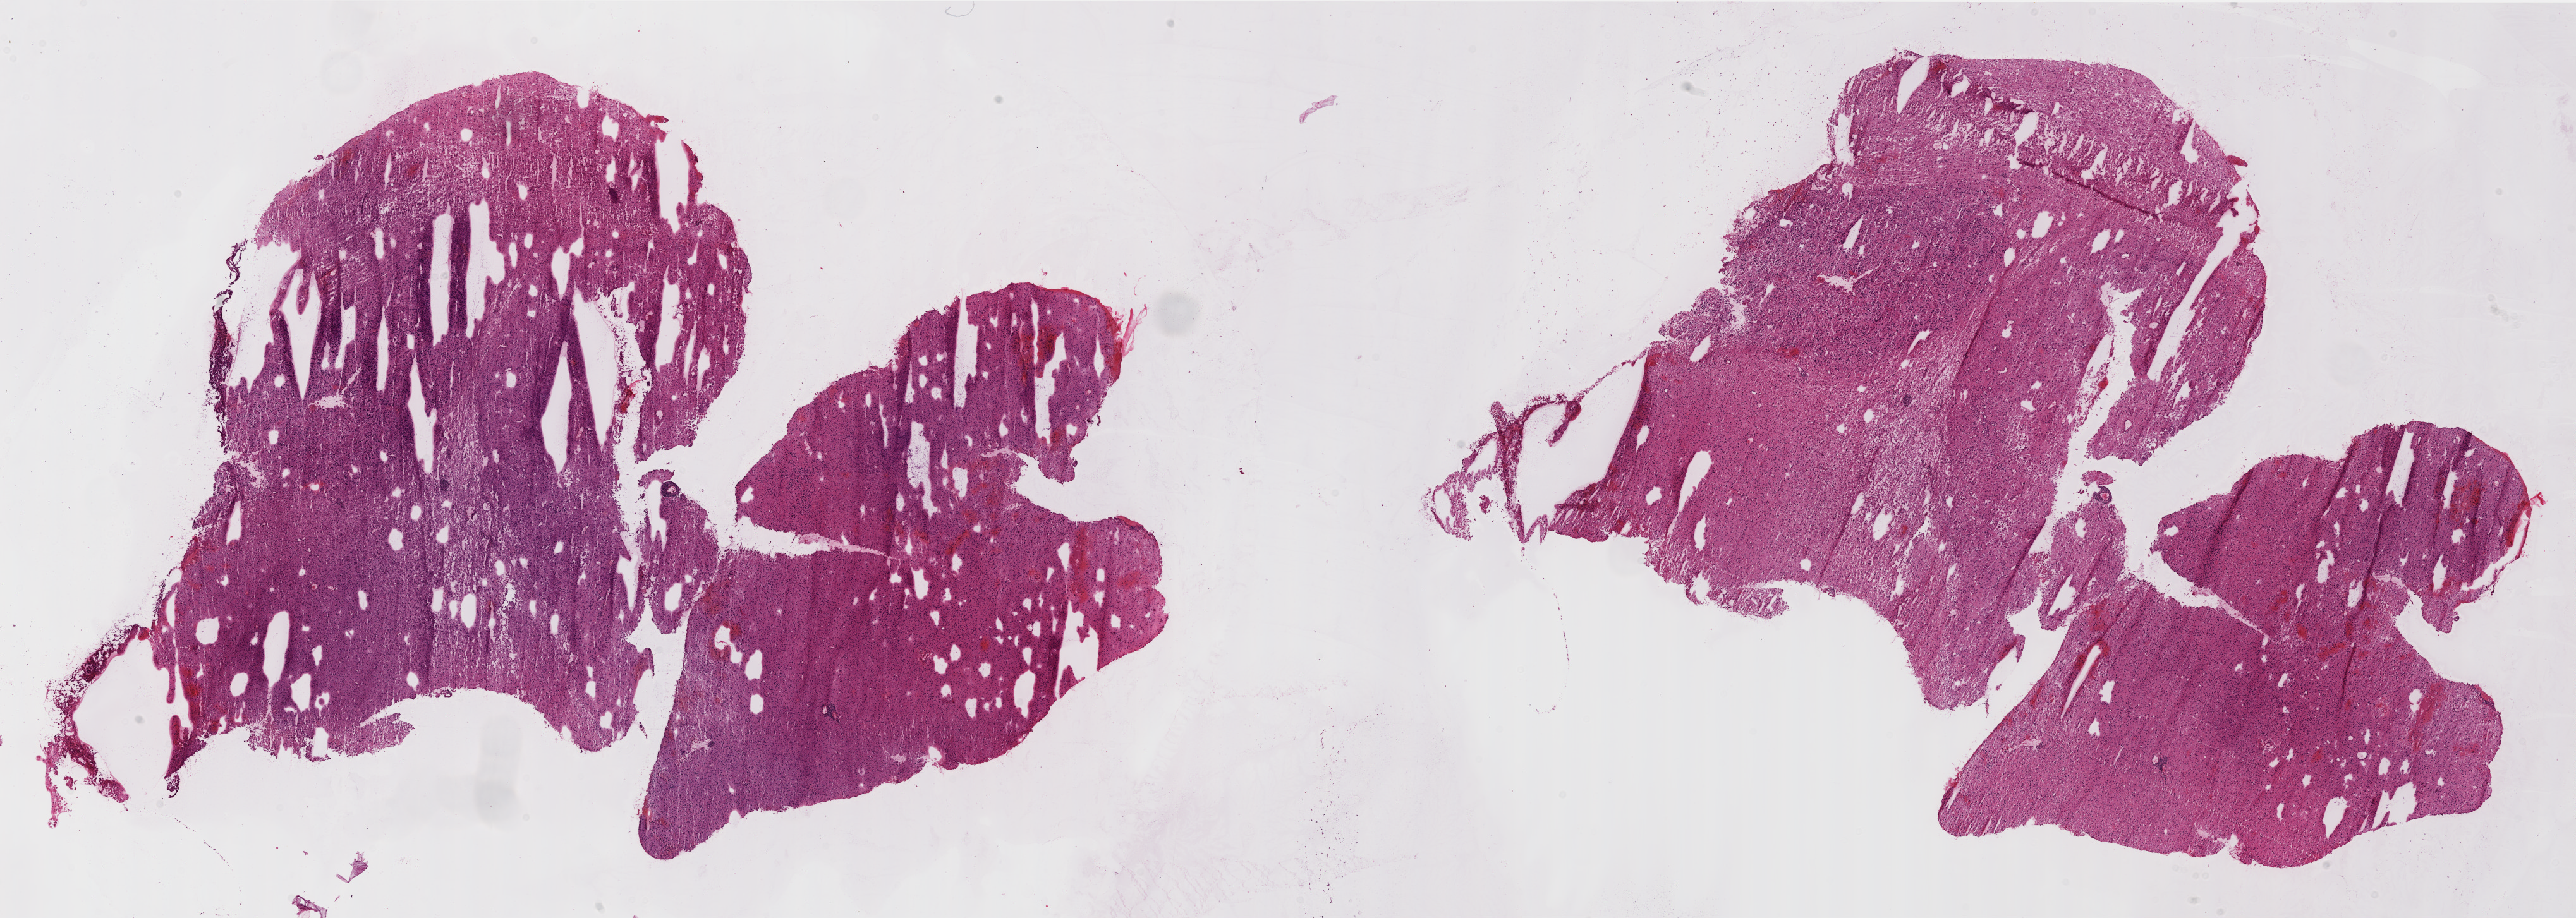
Whole-slide histology image, Hematoxylin and eosin (H&E) stained — shown as a low-resolution overview of the whole scanned area (about 32.8 x 11.7 mm, acquisition: 20x scan). Frozen section. Primary tumour sample from the brain. Female patient; age at initial diagnosis 44 years. Composition of this section per pathologist review: tumour cells 95%, tumour nuclei 95%, normal cells 0%, stromal cells 0%, necrosis 5%. Inflammatory infiltration, as recorded: lymphocyte infiltration 100%.
Histologic diagnosis: Glioblastoma.